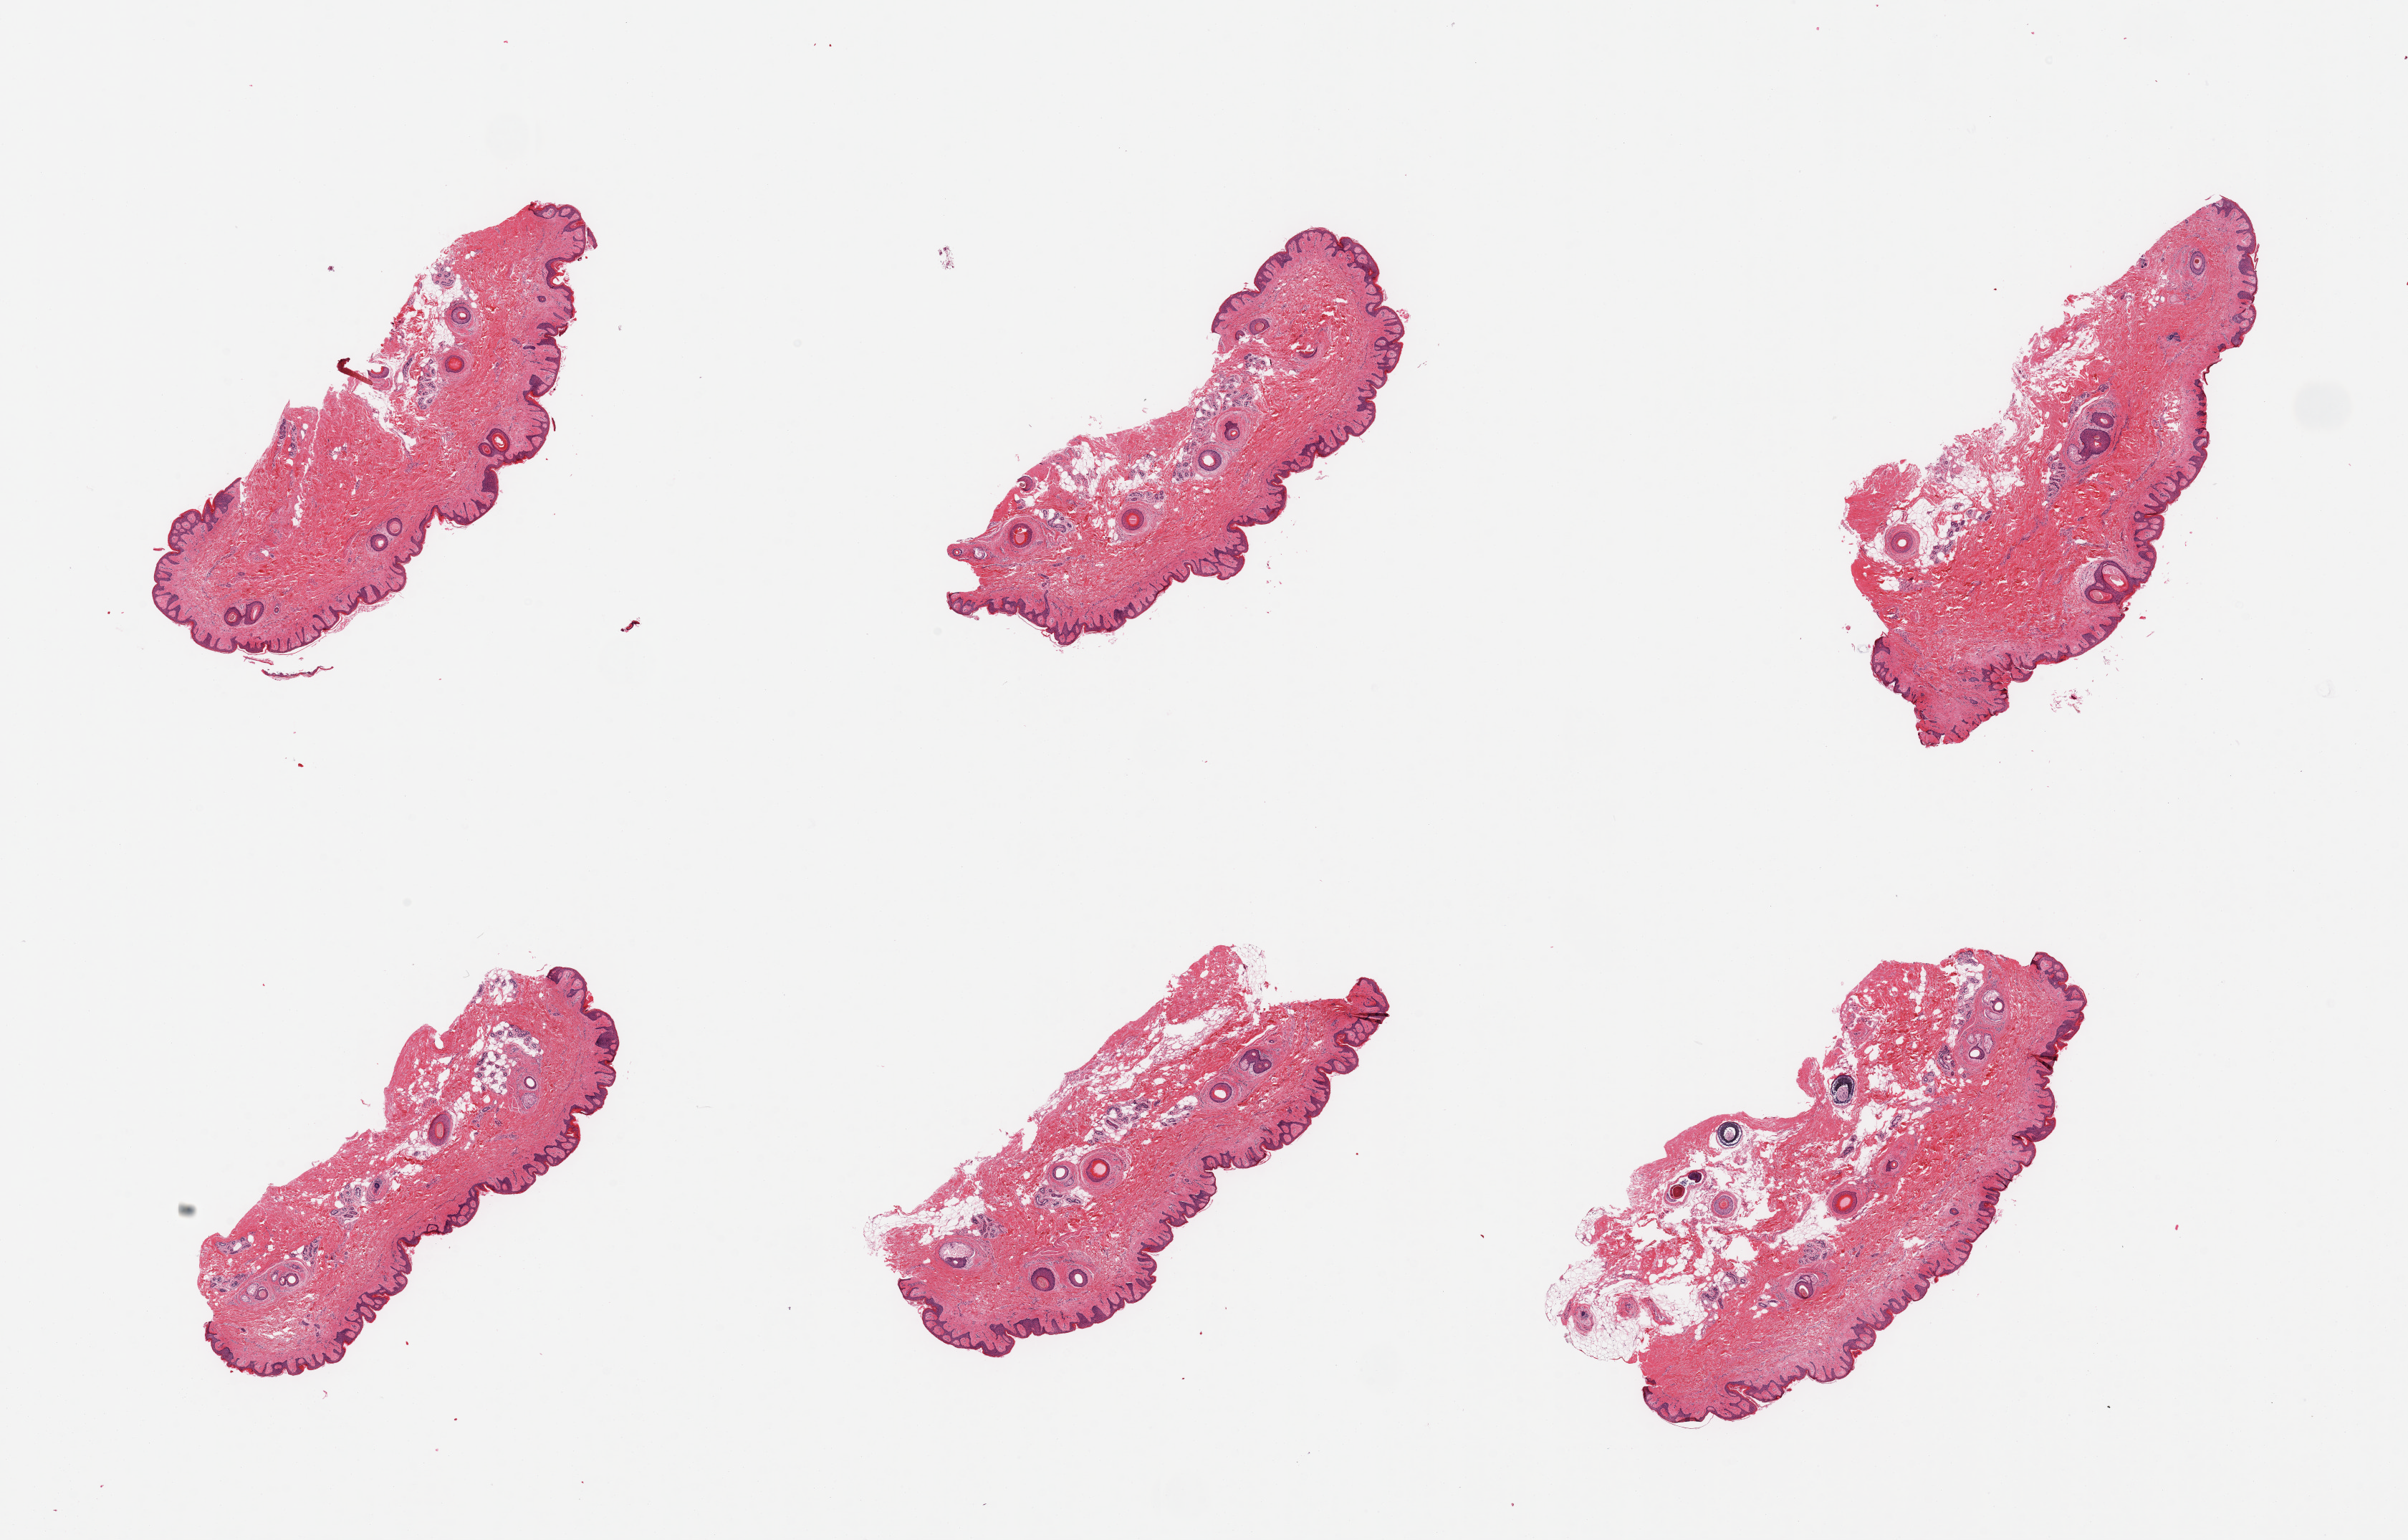
Haematoxylin and eosin whole-slide image, brightfield — low-resolution overview of the scanned area, about 26.6 x 17.0 mm; PAXgene-fixed, paraffin-embedded tissue; section of skin of suprapubic region (target tissue); tissue donor sample. Male donor.
Reviewer comment on this tissue sample: 6 pieces; hair bearing skin with 20% to 40% dermal fat.